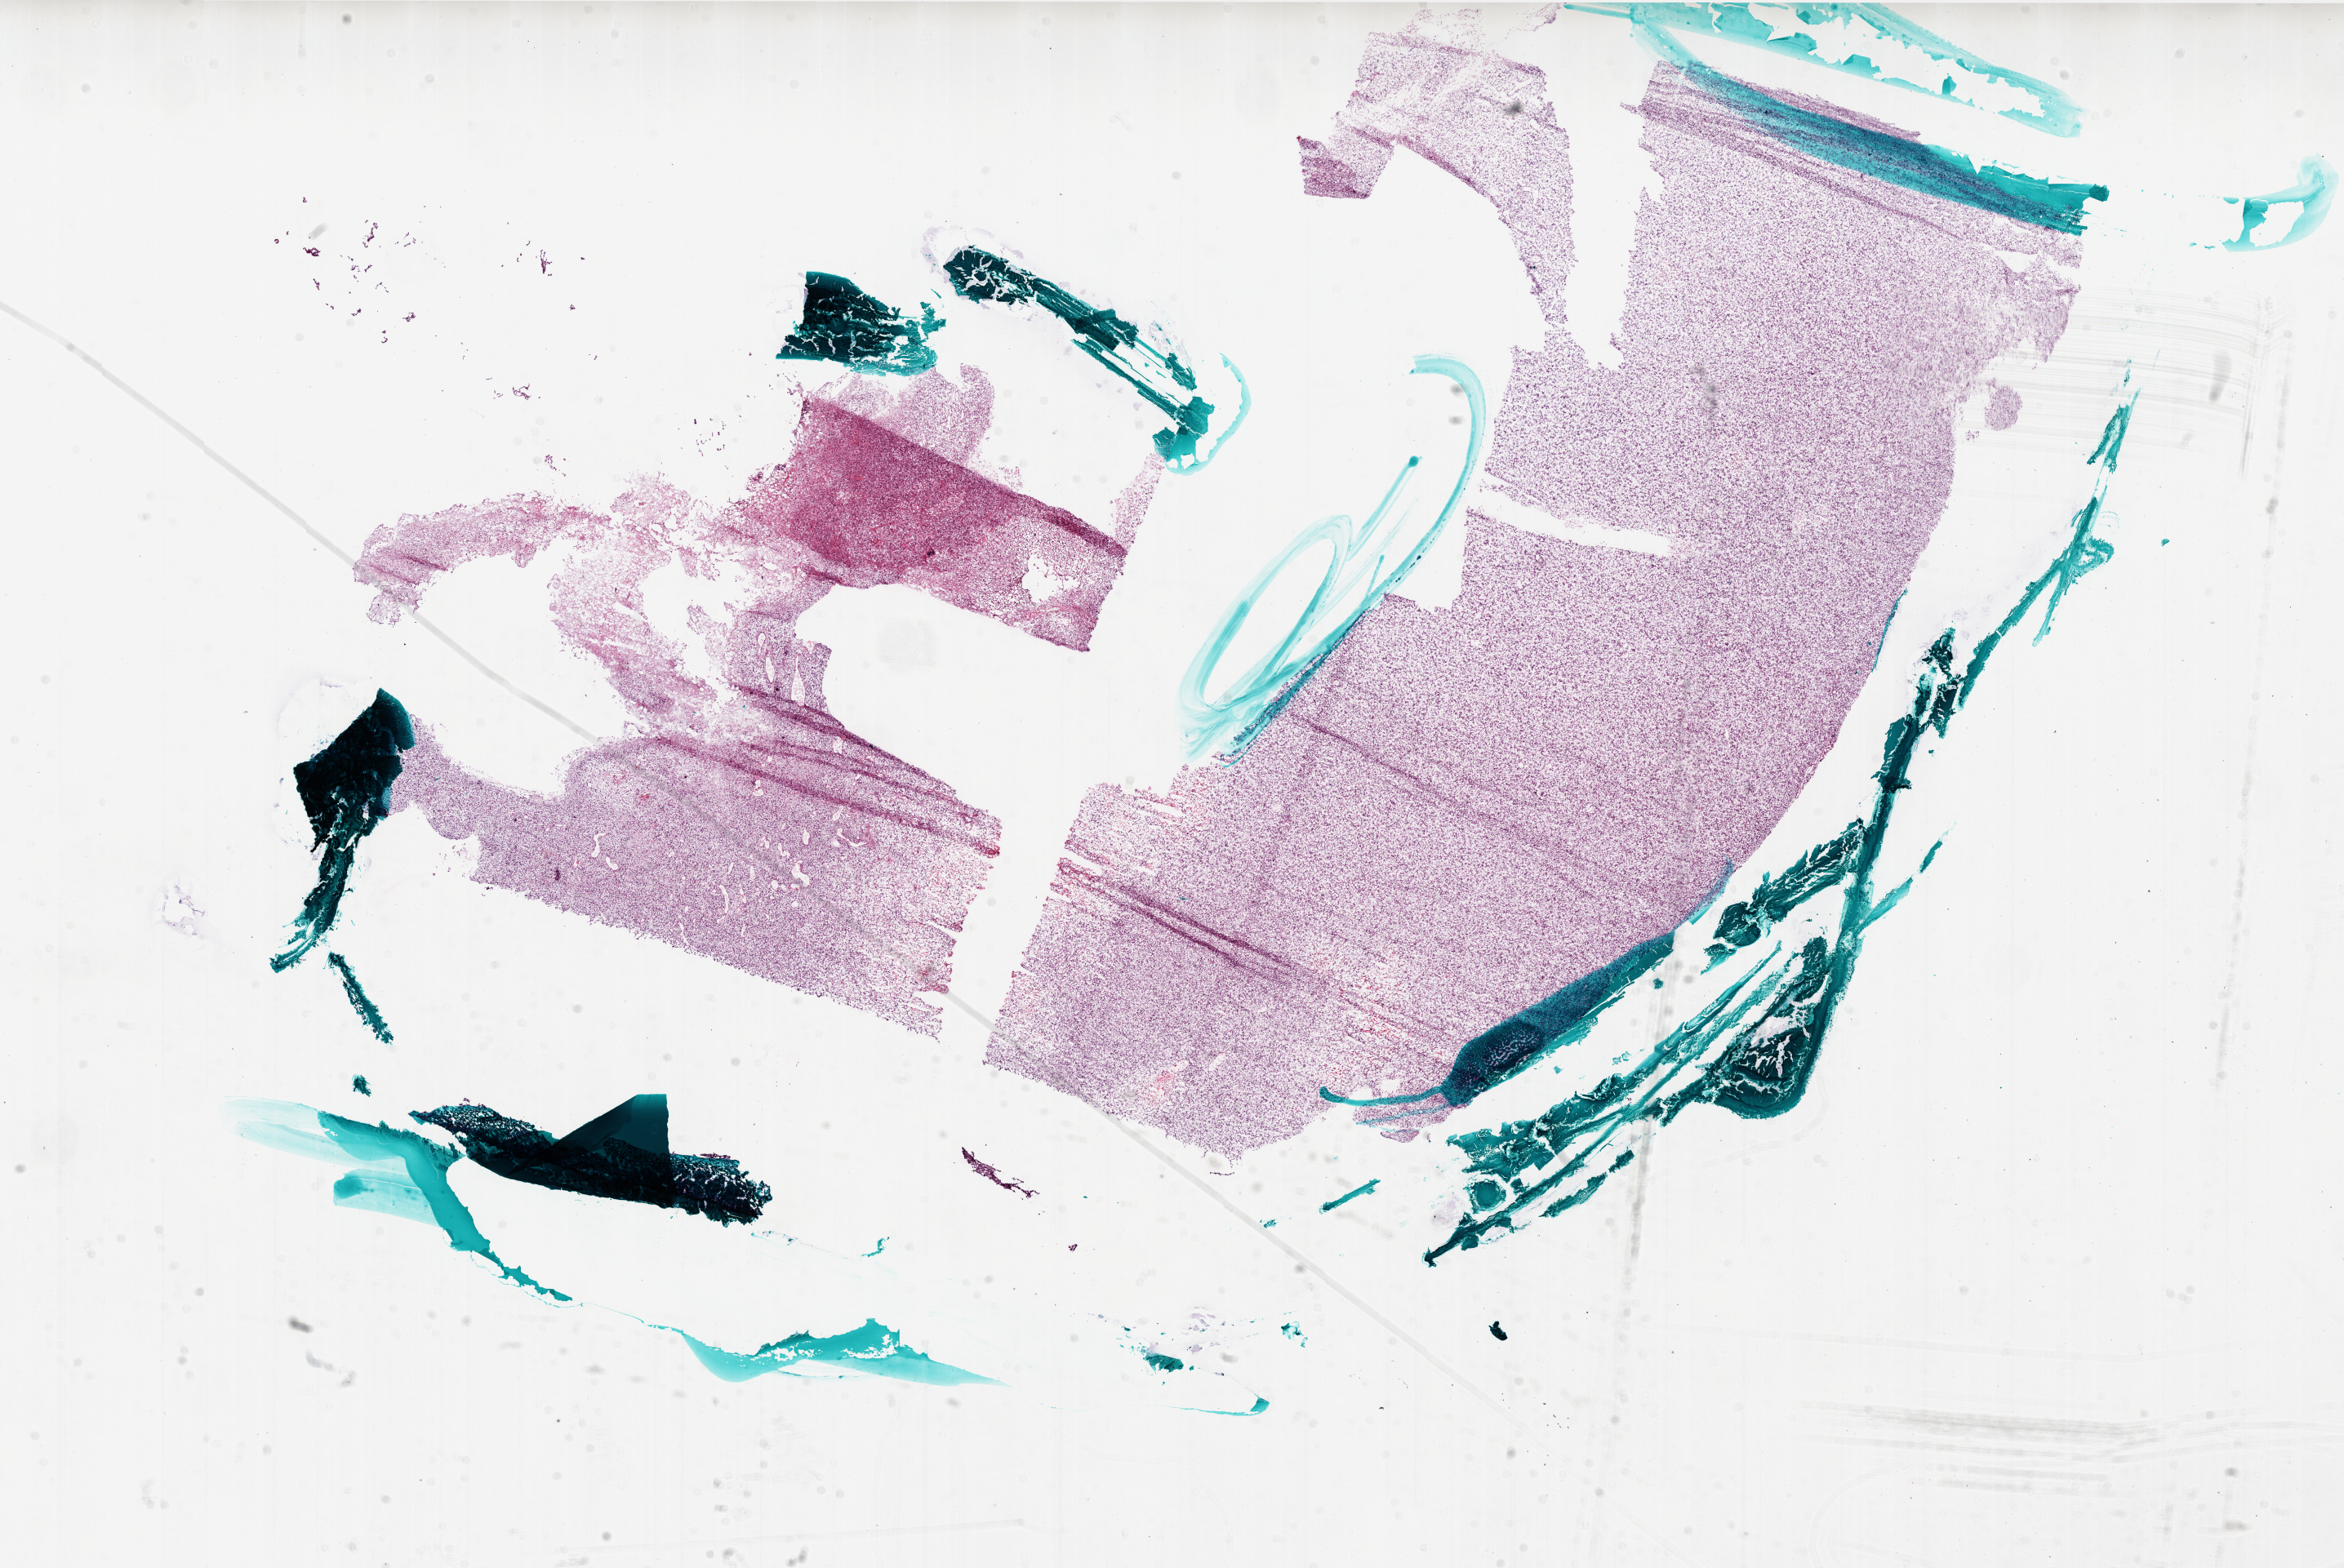
Digitized Hematoxylin and eosin (H&E) stained tissue section (whole slide) — shown as a low-resolution overview of the whole scanned area (about 23.0 x 15.4 mm); frozen section from the bottom of the tissue portion; sample: primary tumour, brain. Patient: male, age at initial diagnosis 51 years. Composition of this section per pathologist review: tumour cells 95%, tumour nuclei 100%, normal cells 0%, stromal cells 0%, necrosis 5%.
* diagnosis: Glioblastoma